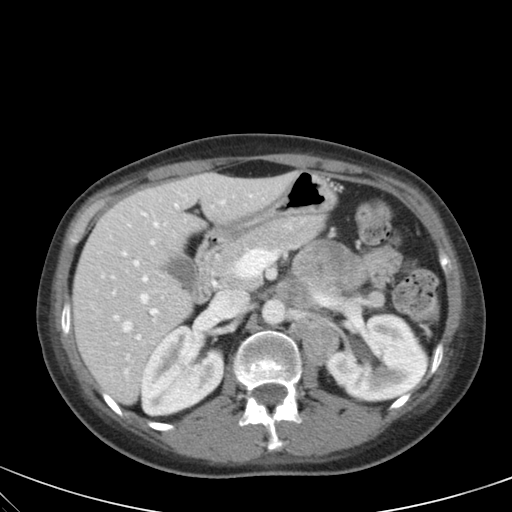
Contrast-enhanced abdominal CT, one axial slice. Position 31 of 59 along the scan axis. Intravenous contrast given. Soft-tissue window (W 400 / L 40 HU). 4 mm slice thickness. 512 × 512 image matrix, field of view 350 × 350 mm. Female patient, age 28 years. Case-level facts recorded for this patient, not image findings: diagnosis: adrenocortical carcinoma; tumour side: left adrenal; tumour size at pathology: 7 cm.
Annotated regions visible in this slice (semi-automatic segmentation, software-assisted and operator-edited):
- mass: bounding box [x1, y1, x2, y2] px = [294, 241, 368, 288]